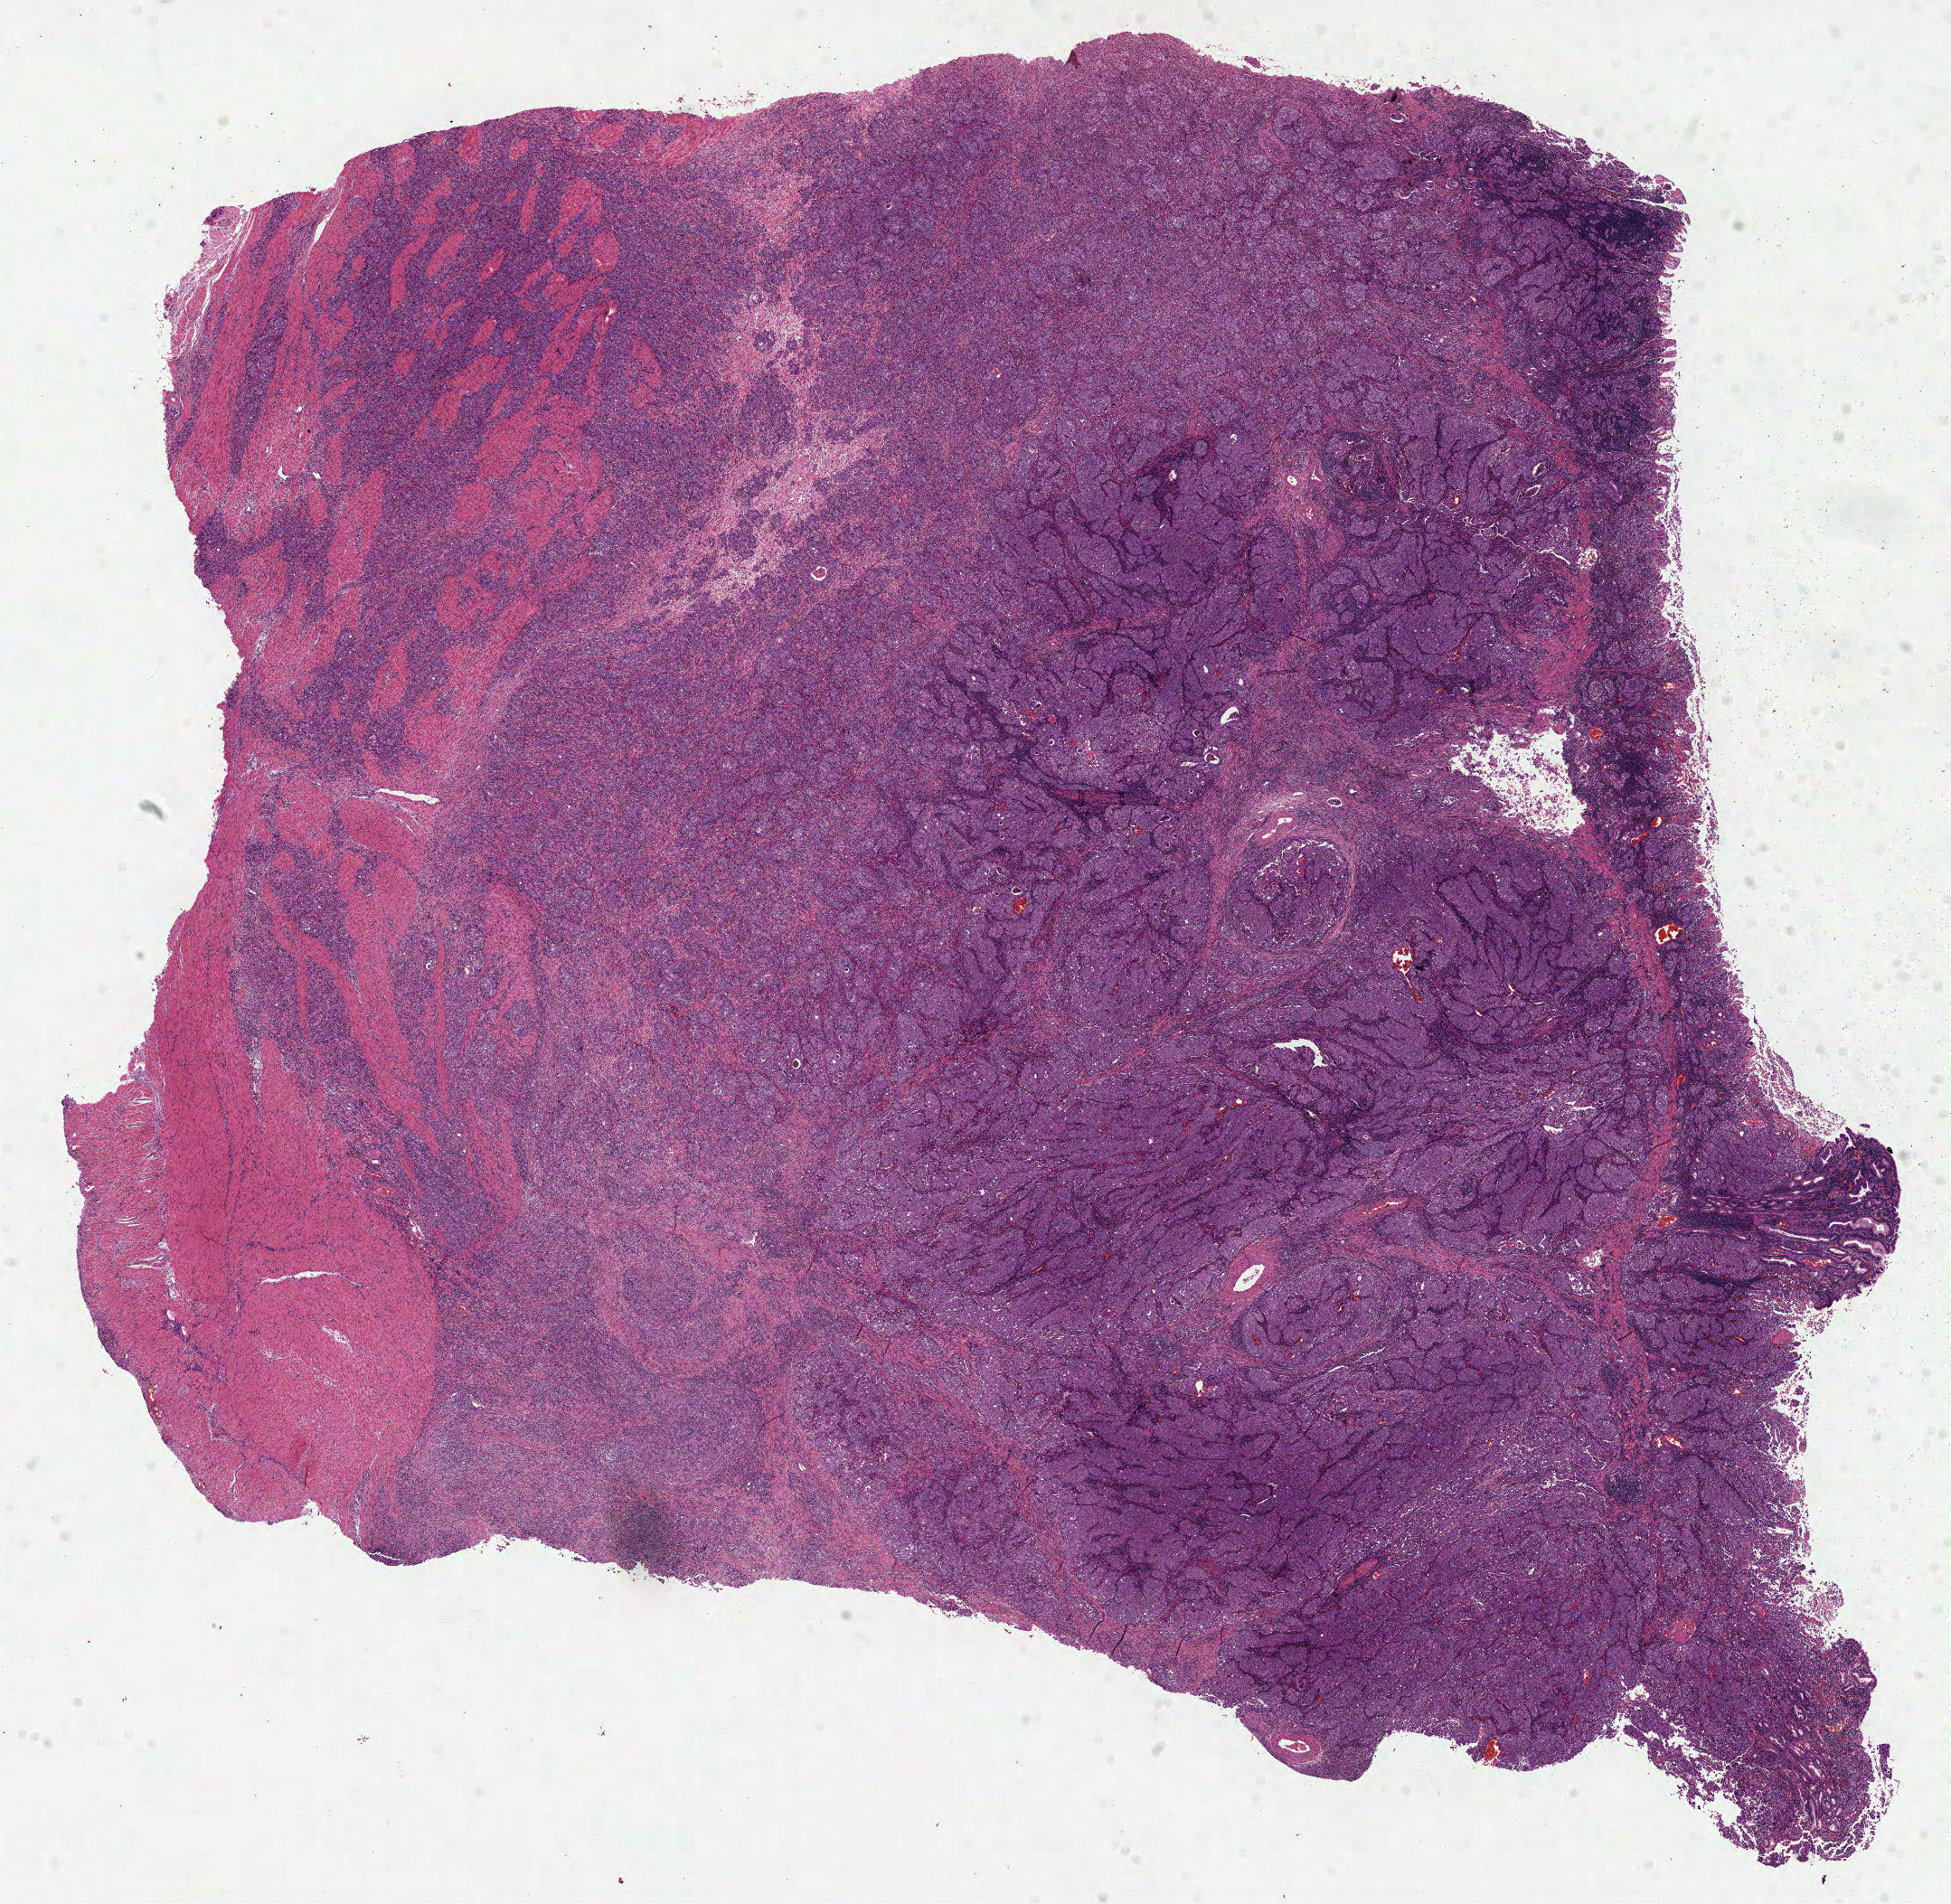
Digitized H&E-stained tissue section (whole slide), shown as a low-resolution overview of the whole scanned area (about 17.4 x 17.0 mm, acquisition: 40x scan), formalin-fixed paraffin-embedded (FFPE) diagnostic section, sample: primary tumour, stomach. Patient: male, age at initial diagnosis 69 years. Histologic grade: G3 (poorly differentiated).
AJCC pathologic stage: IIIA (6th edition). Pathologic diagnosis: Adenocarcinoma, NOS (gastric antrum).